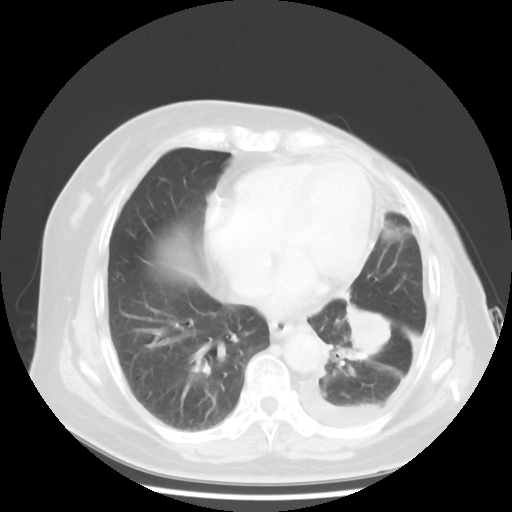
Chest CT, one axial slice; position 16 of 48 along the scan axis; reconstruction kernel STANDARD; 120 kVp; lung window (W 1500 / L -600 HU); 512 × 512 image matrix, field of view 360 × 360 mm. Patient: female, 63 years. Case-level facts recorded for this patient, not image findings: clinical TNM (as recorded): T2 N0 M1.
Structures marked on this image (rectangle marked by the reading radiologist):
- lung tumour (recorded histology: adenocarcinoma): box from (x=329, y=303) to (x=394, y=366) px